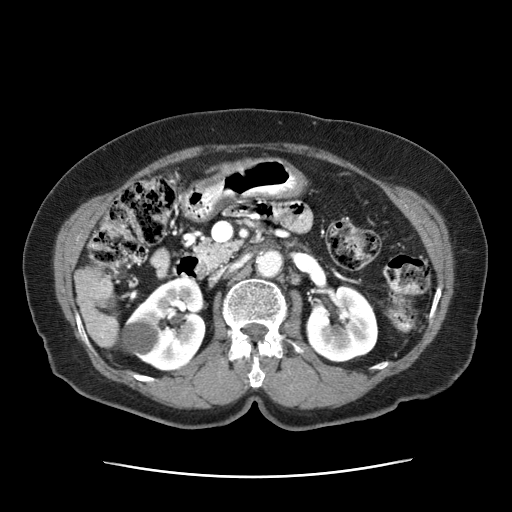
Contrast-enhanced abdominal CT (liver protocol), one axial slice; slice 12 of 63 in the series (ordered by position); 120 kVp; soft-tissue window (W 400 / L 40 HU); 512 × 512 image matrix, field of view 360 × 360 mm. Female patient, age 79 years. Case-level facts recorded for this patient, not image findings: diagnosis: hepatocellular carcinoma (patient treated with transarterial chemoembolisation; whether this scan precedes or follows treatment is not stated here); TNM stage (as recorded): Stage-II; Child-Pugh class: B; tumour size: 5 cm.
Annotated regions visible in this slice (semi-automatic segmentation, software-assisted and operator-edited):
- abdominal aorta: box from (x=256, y=248) to (x=284, y=276) px
- liver parenchyma outside the tumour (the mass and vessels are separate outlines, so this box may not span the whole liver): (x=74, y=266)–(x=118, y=347)